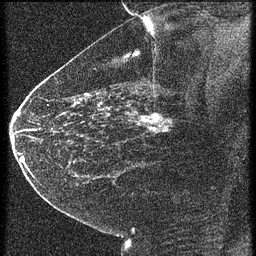
Breast MRI (dynamic contrast-enhanced), one sagittal slice. 4 images stored at this slice position (order not interpretable as contrast timing). 1.5 T. TE 4.2 ms, TR 21.3 ms. 1.5 mm slice thickness. 256 × 256 image matrix, field of view 180 × 180 mm. Female patient, age 43 years. From the clinical record (not read from this slice): setting: breast cancer imaged before/during neoadjuvant chemotherapy; receptor status: HER2-positive.
Outlined on this slice (semi-automatic segmentation, software-assisted and operator-edited):
- analysis volume of interest (the breast-tissue region the enhancement analysis was run in; not a lesion): bounding box [x1, y1, x2, y2] px = [122, 100, 187, 151]
- tumour enhancement mask (voxels above the 90 % enhancement threshold inside the analysis volume of interest): [138, 112, 169, 133]